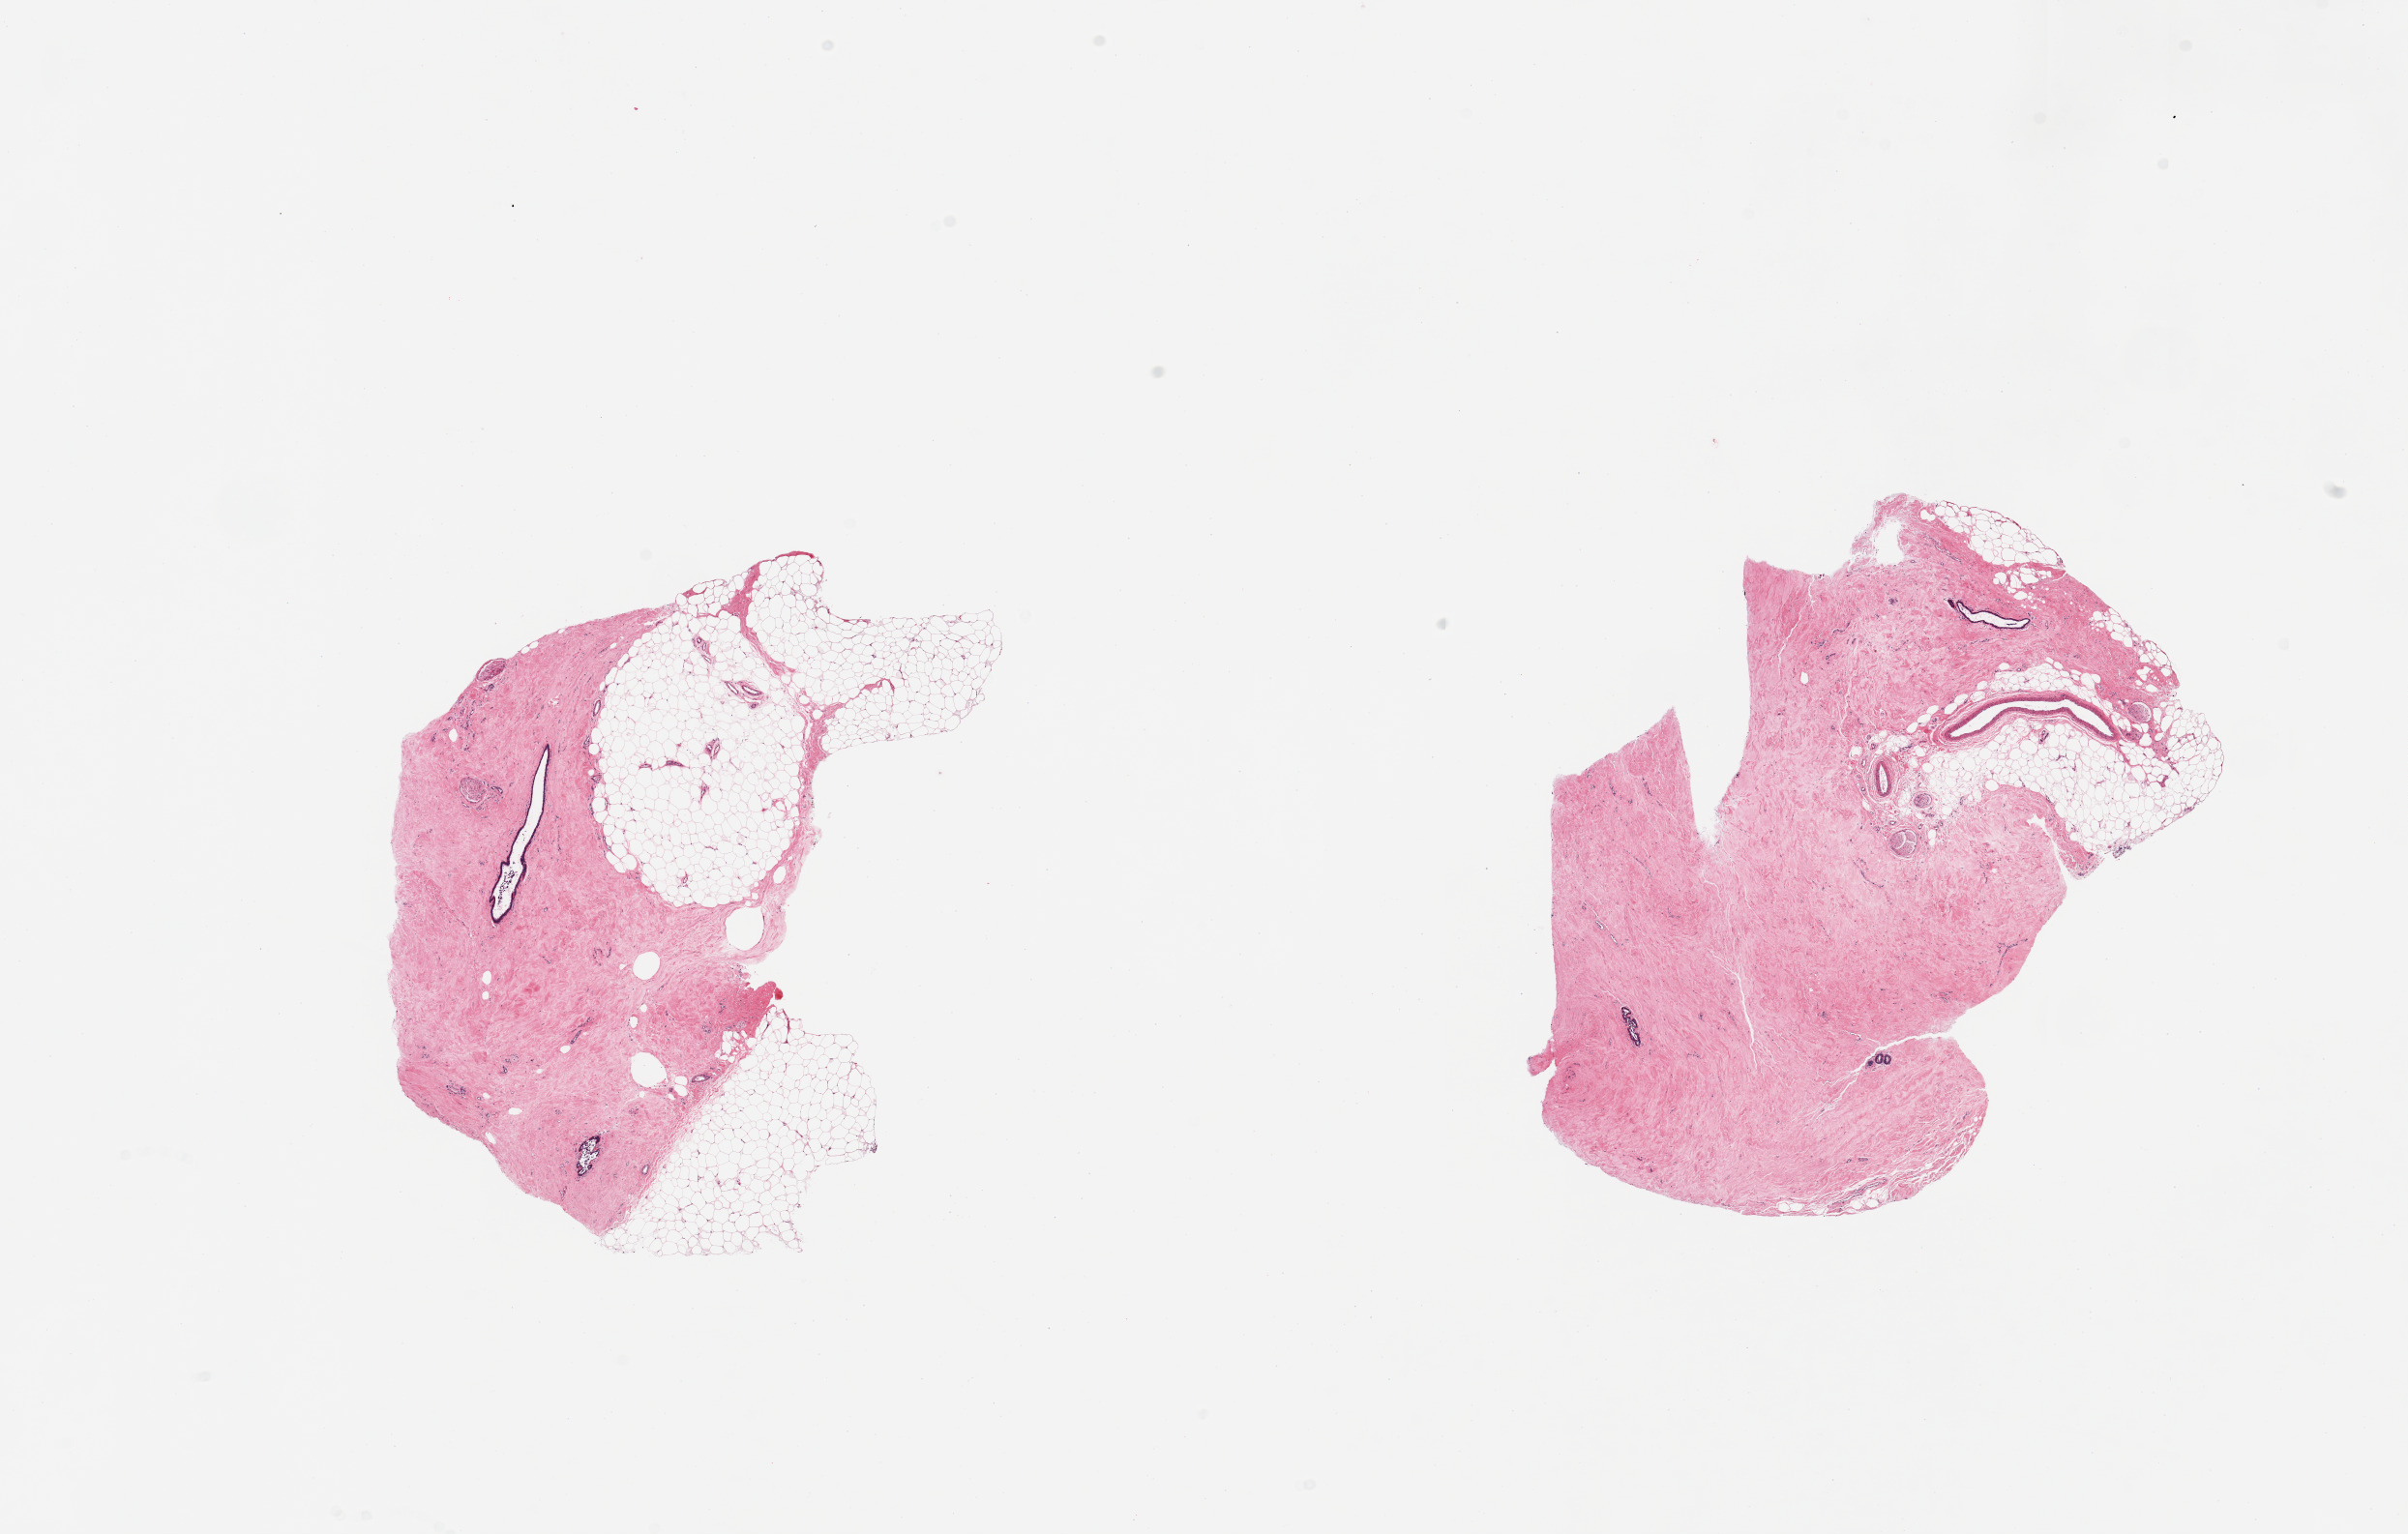
Digitized H&E-stained section, whole scanned area (about 19.7 x 12.5 mm, from a 20x scan) shown as a low-resolution overview. PAXgene-fixed, paraffin-embedded tissue. Sampled site (target tissue): breast. Tissue donor sample. Male donor.
Pathologist's review note for this sample: 2 pieces, gynecomastoid hyperplasia, rep ductal elements.